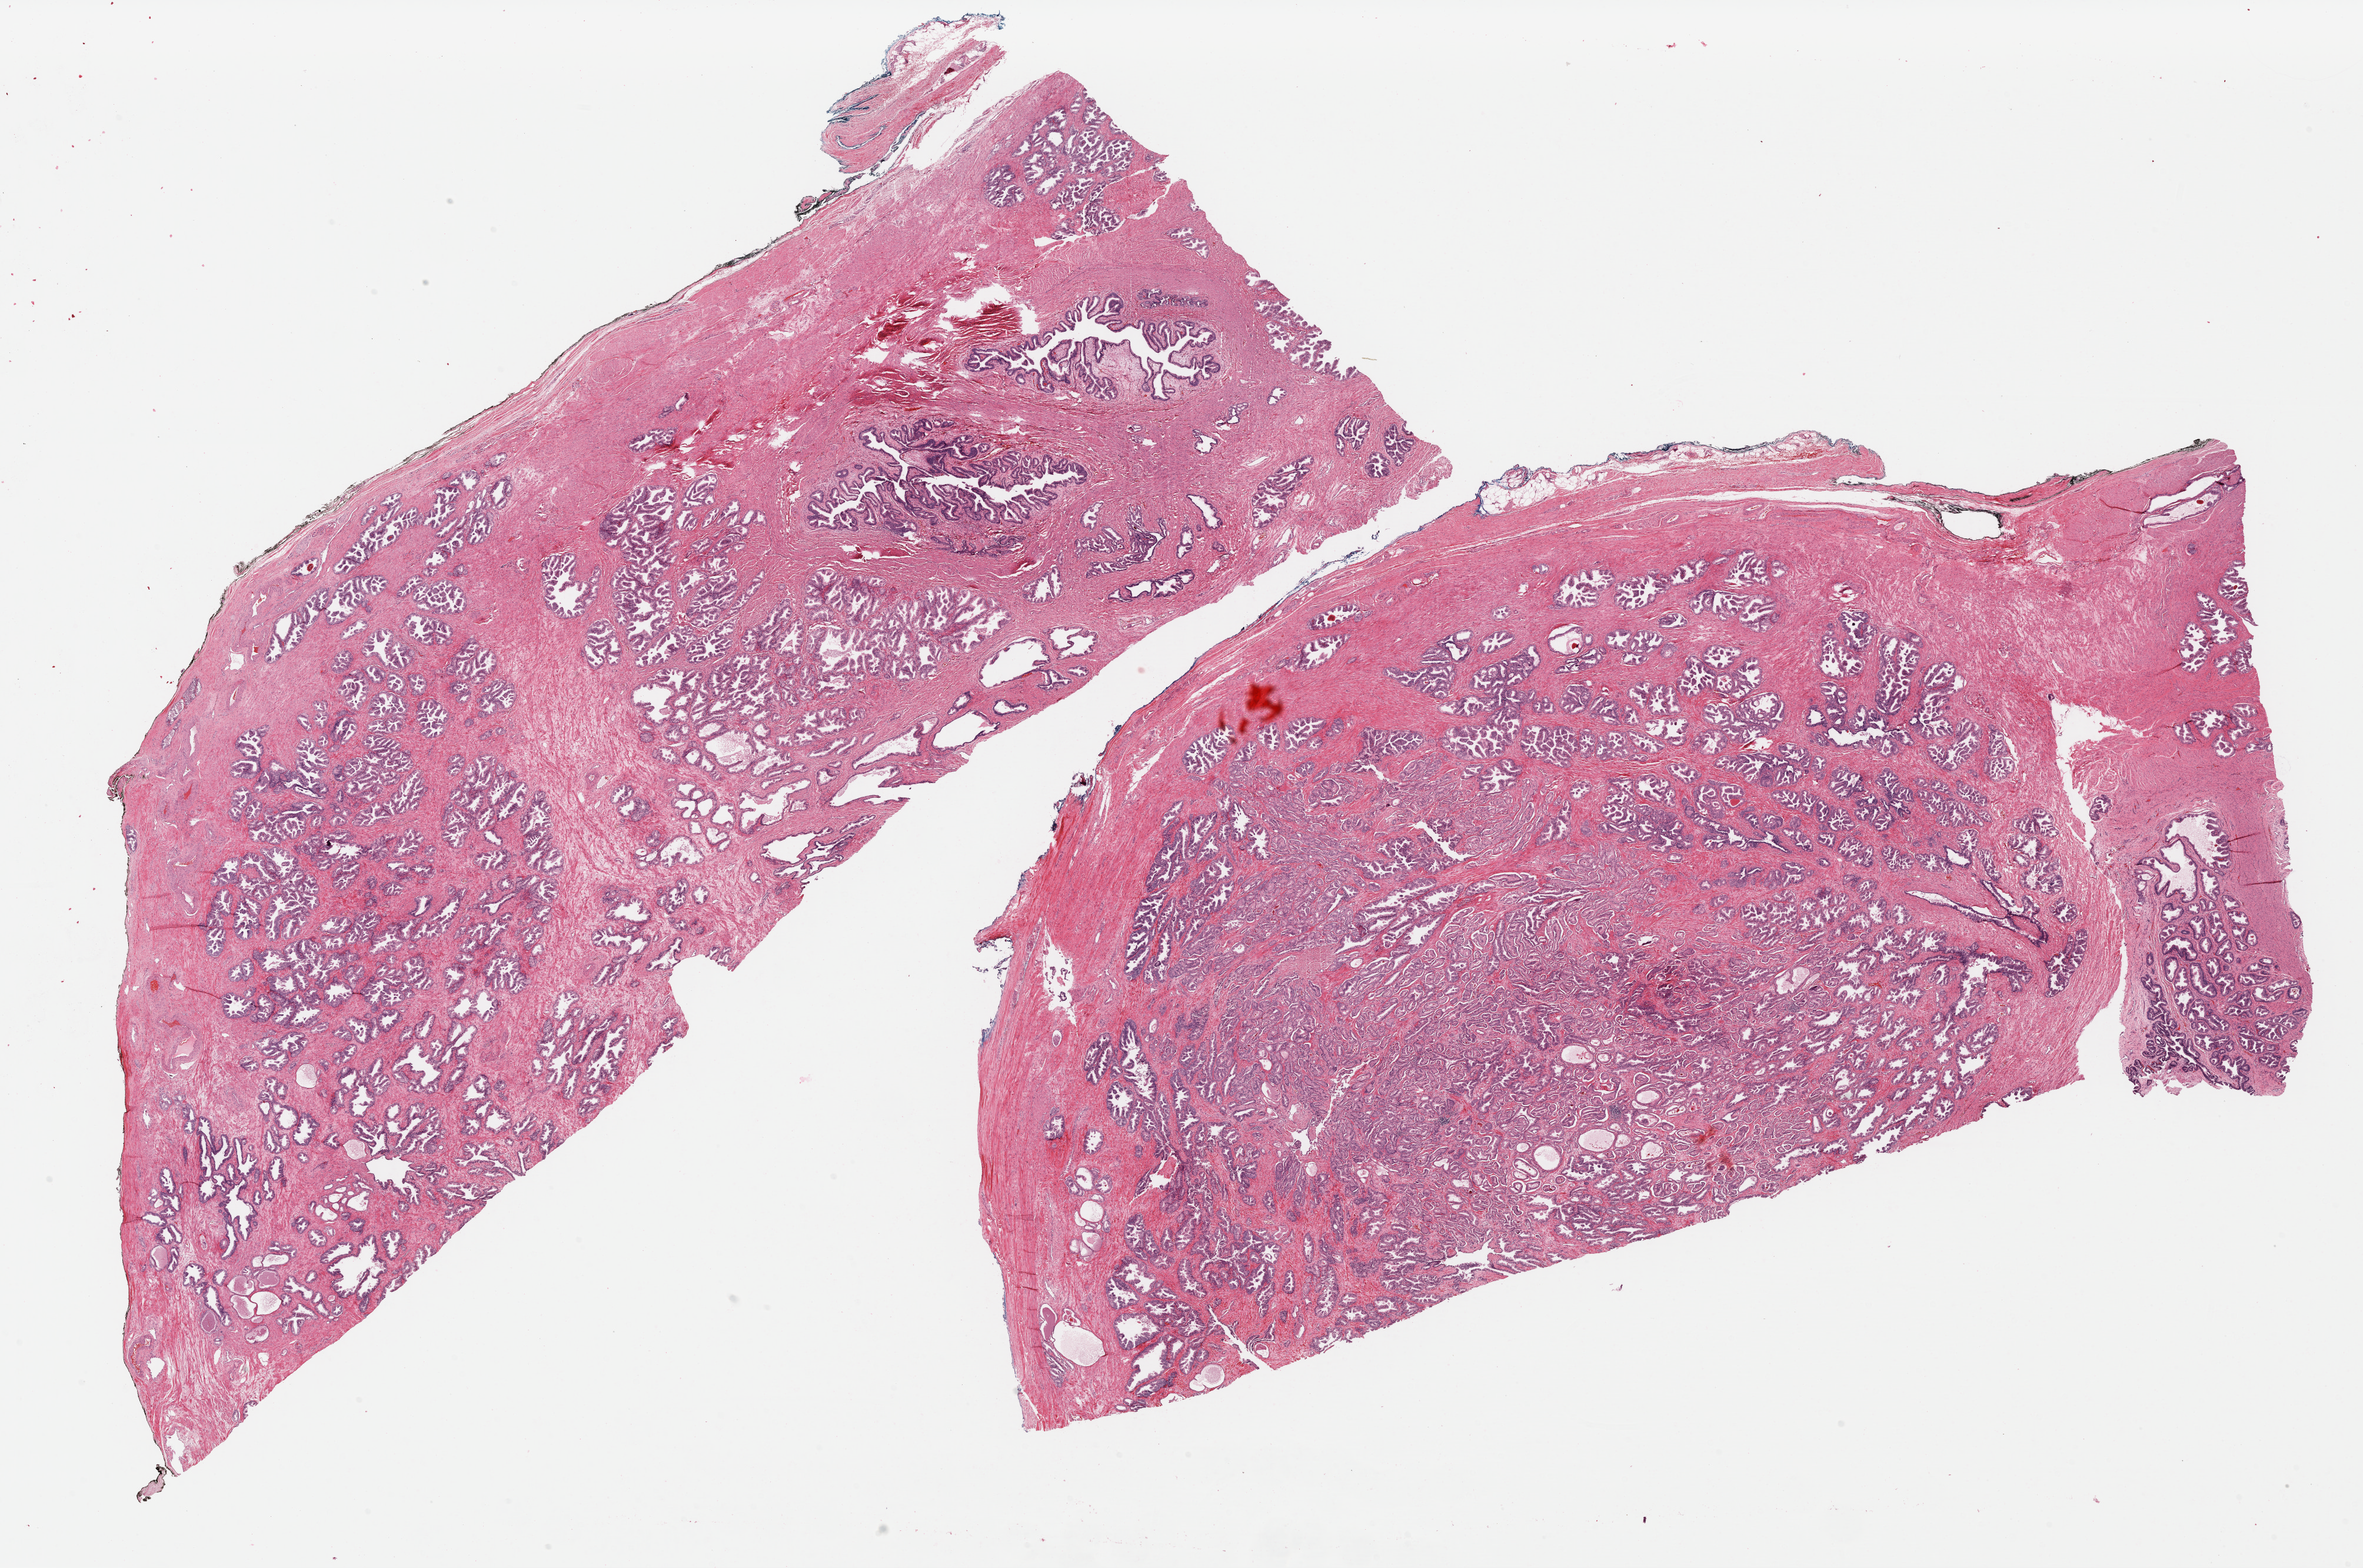
Digitized Hematoxylin and eosin (H&E) stained tissue section (whole slide), a low-resolution overview of the entire scanned area, about 31.6 x 20.9 mm (from a 40x scan); formalin-fixed paraffin-embedded (FFPE) diagnostic section; sample: primary tumour, prostate. Male patient; age at initial diagnosis 47 years. Gleason score: 7 (3+4).
- diagnosis: Acinar cell carcinoma (prostate gland)
- laterality: bilateral
- lymph nodes positive (case pathology): 0 of 4 examined